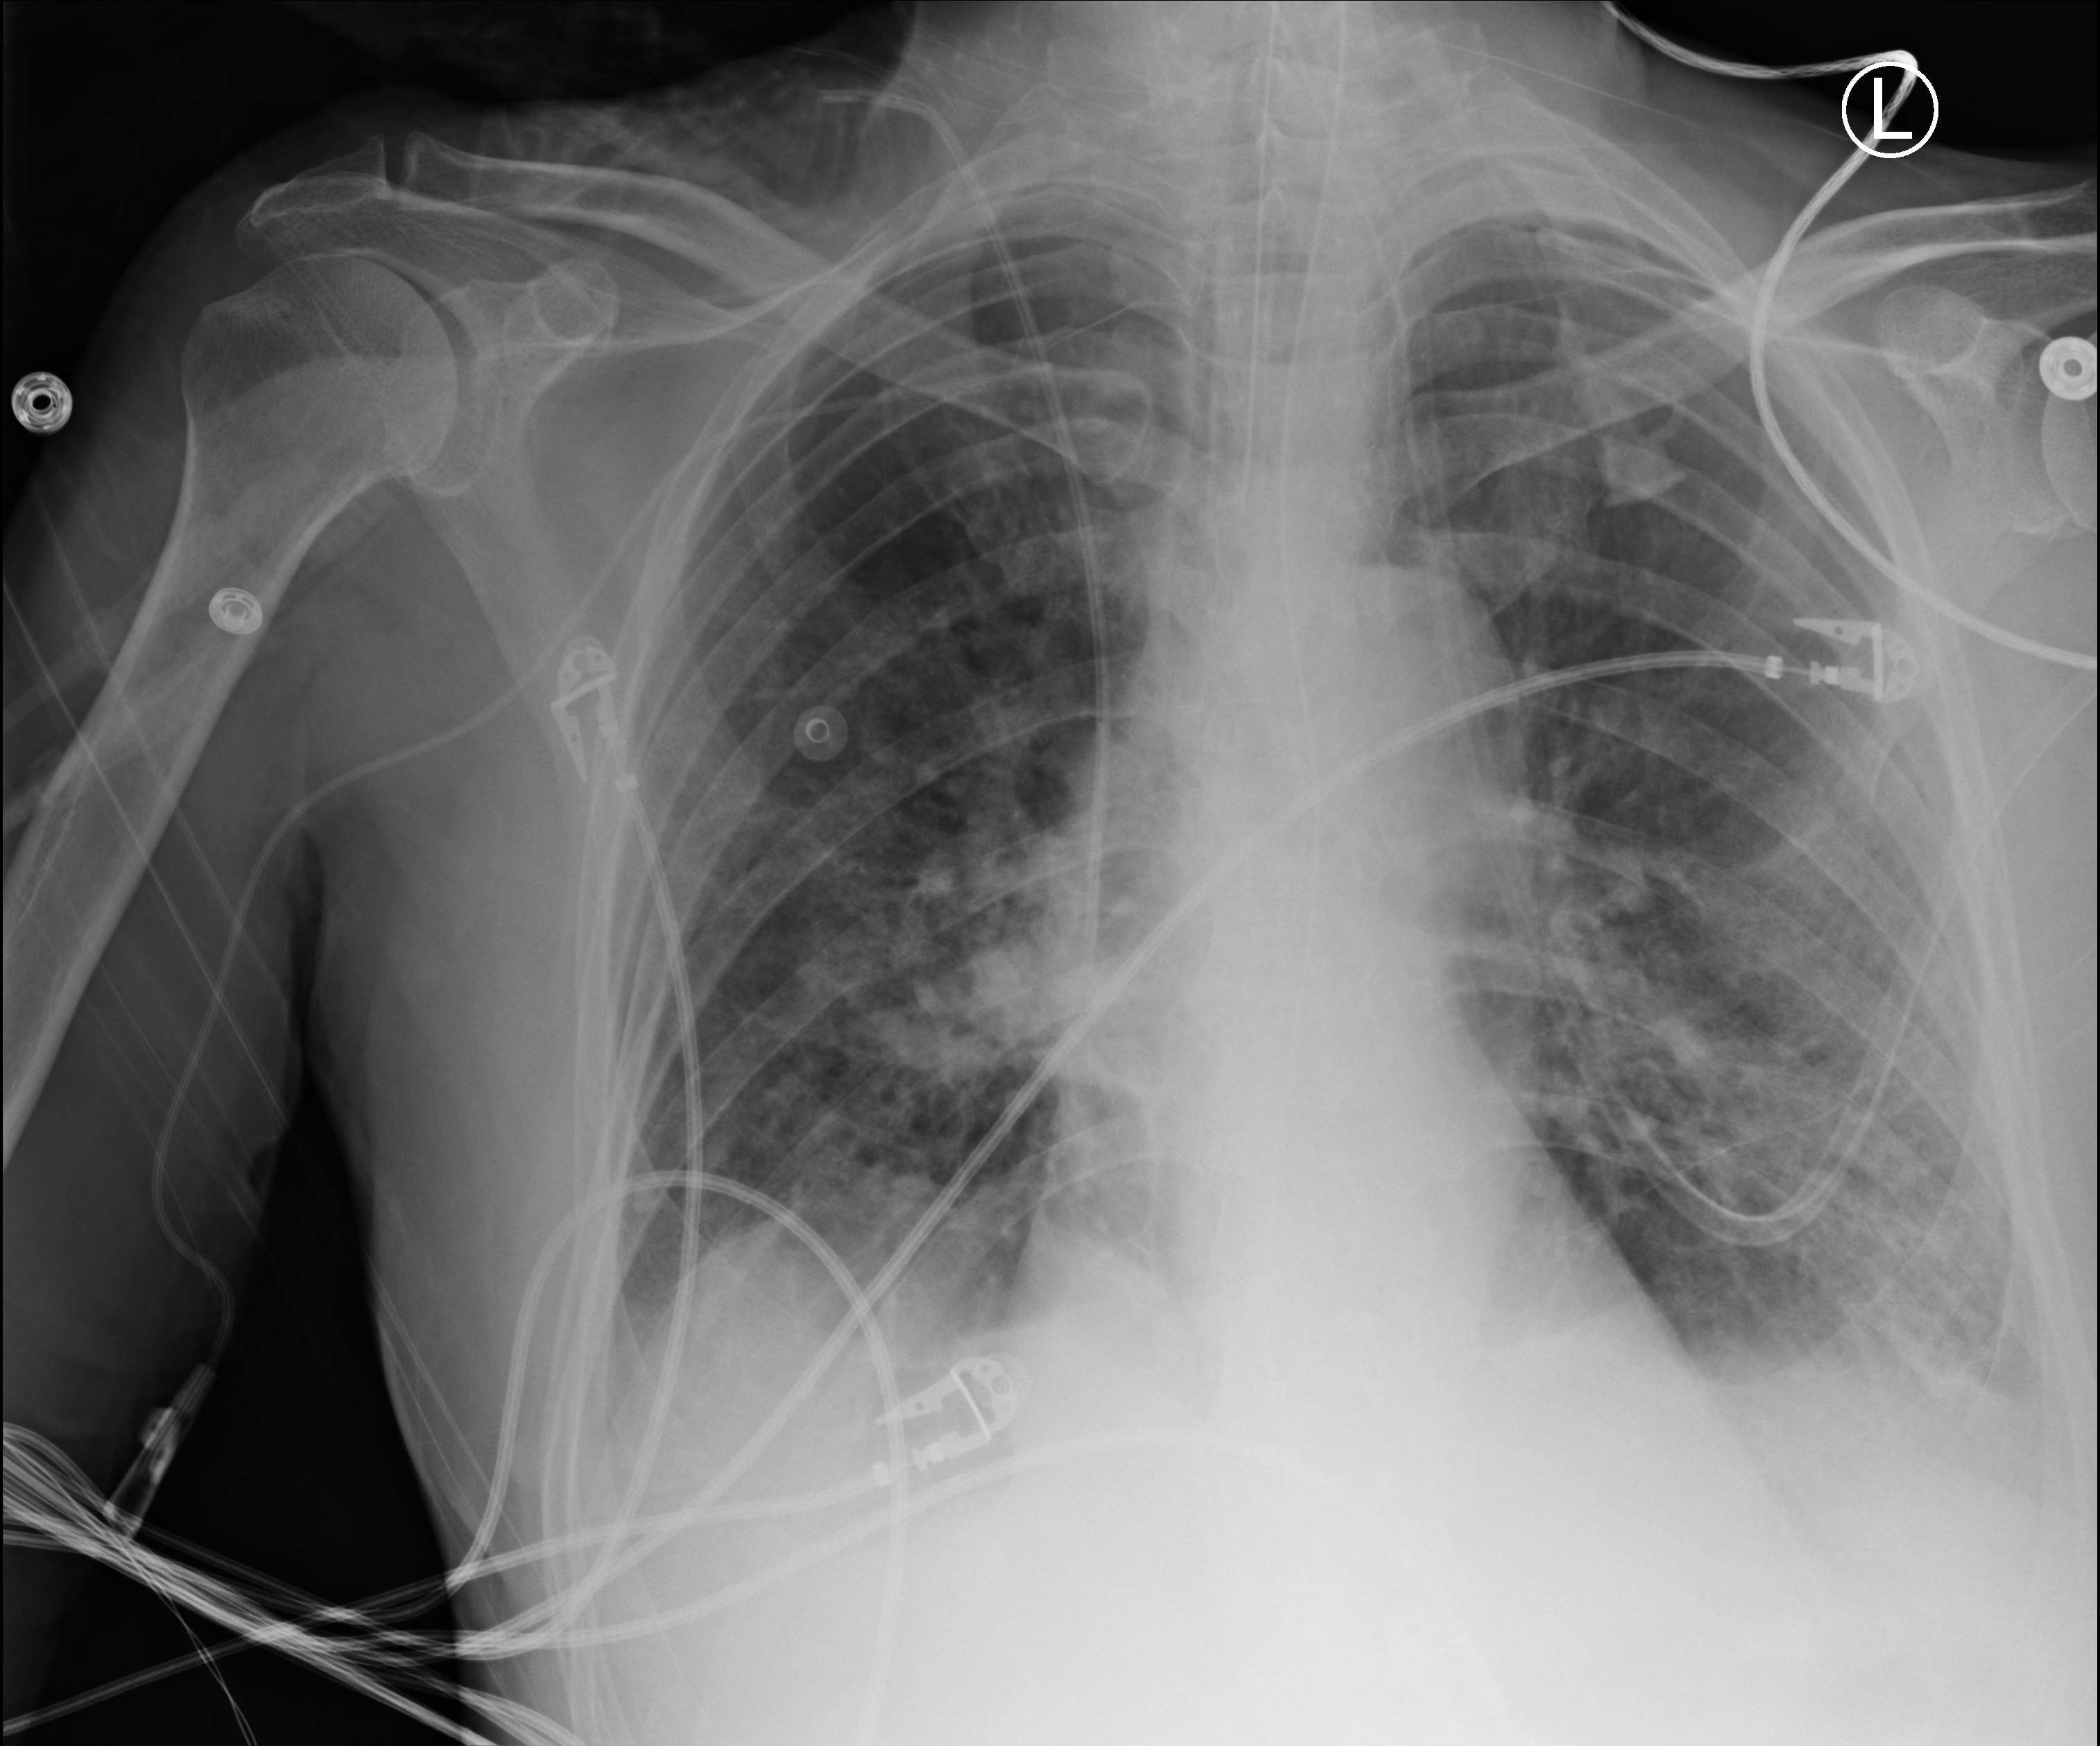
Chest X-ray (portable); anteroposterior (AP) projection. Male patient hospitalised with COVID-19, age 75–90 years.
Hospital-stay facts (about this admission, not read from this image; timing relative to this image not recorded):
- mechanically ventilated during this hospital stay: yes